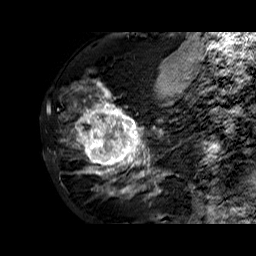
Breast MRI (dynamic contrast-enhanced), one sagittal slice. Slice 25 of 60 in the series (ordered by position). Dynamic contrast-enhanced series, time point 2 of 6 at this slice position (early post-contrast). 1.5 T. TE 6.3 ms, TR 32.4 ms. 4 mm slice thickness. 256 × 256 image matrix, field of view 200 × 200 mm. Female patient. From the clinical record (not read from this slice): setting: breast cancer imaged before/during neoadjuvant chemotherapy; receptor status: HR-positive, HER2-negative.
Annotated regions visible in this slice (semi-automatic segmentation, software-assisted and operator-edited):
- analysis volume of interest (the breast-tissue region the enhancement analysis was run in; not a lesion): box from (x=68, y=72) to (x=177, y=182) px
- tumour enhancement mask (voxels above the 100 % enhancement threshold inside the analysis volume of interest): (x=78, y=85)–(x=166, y=178)